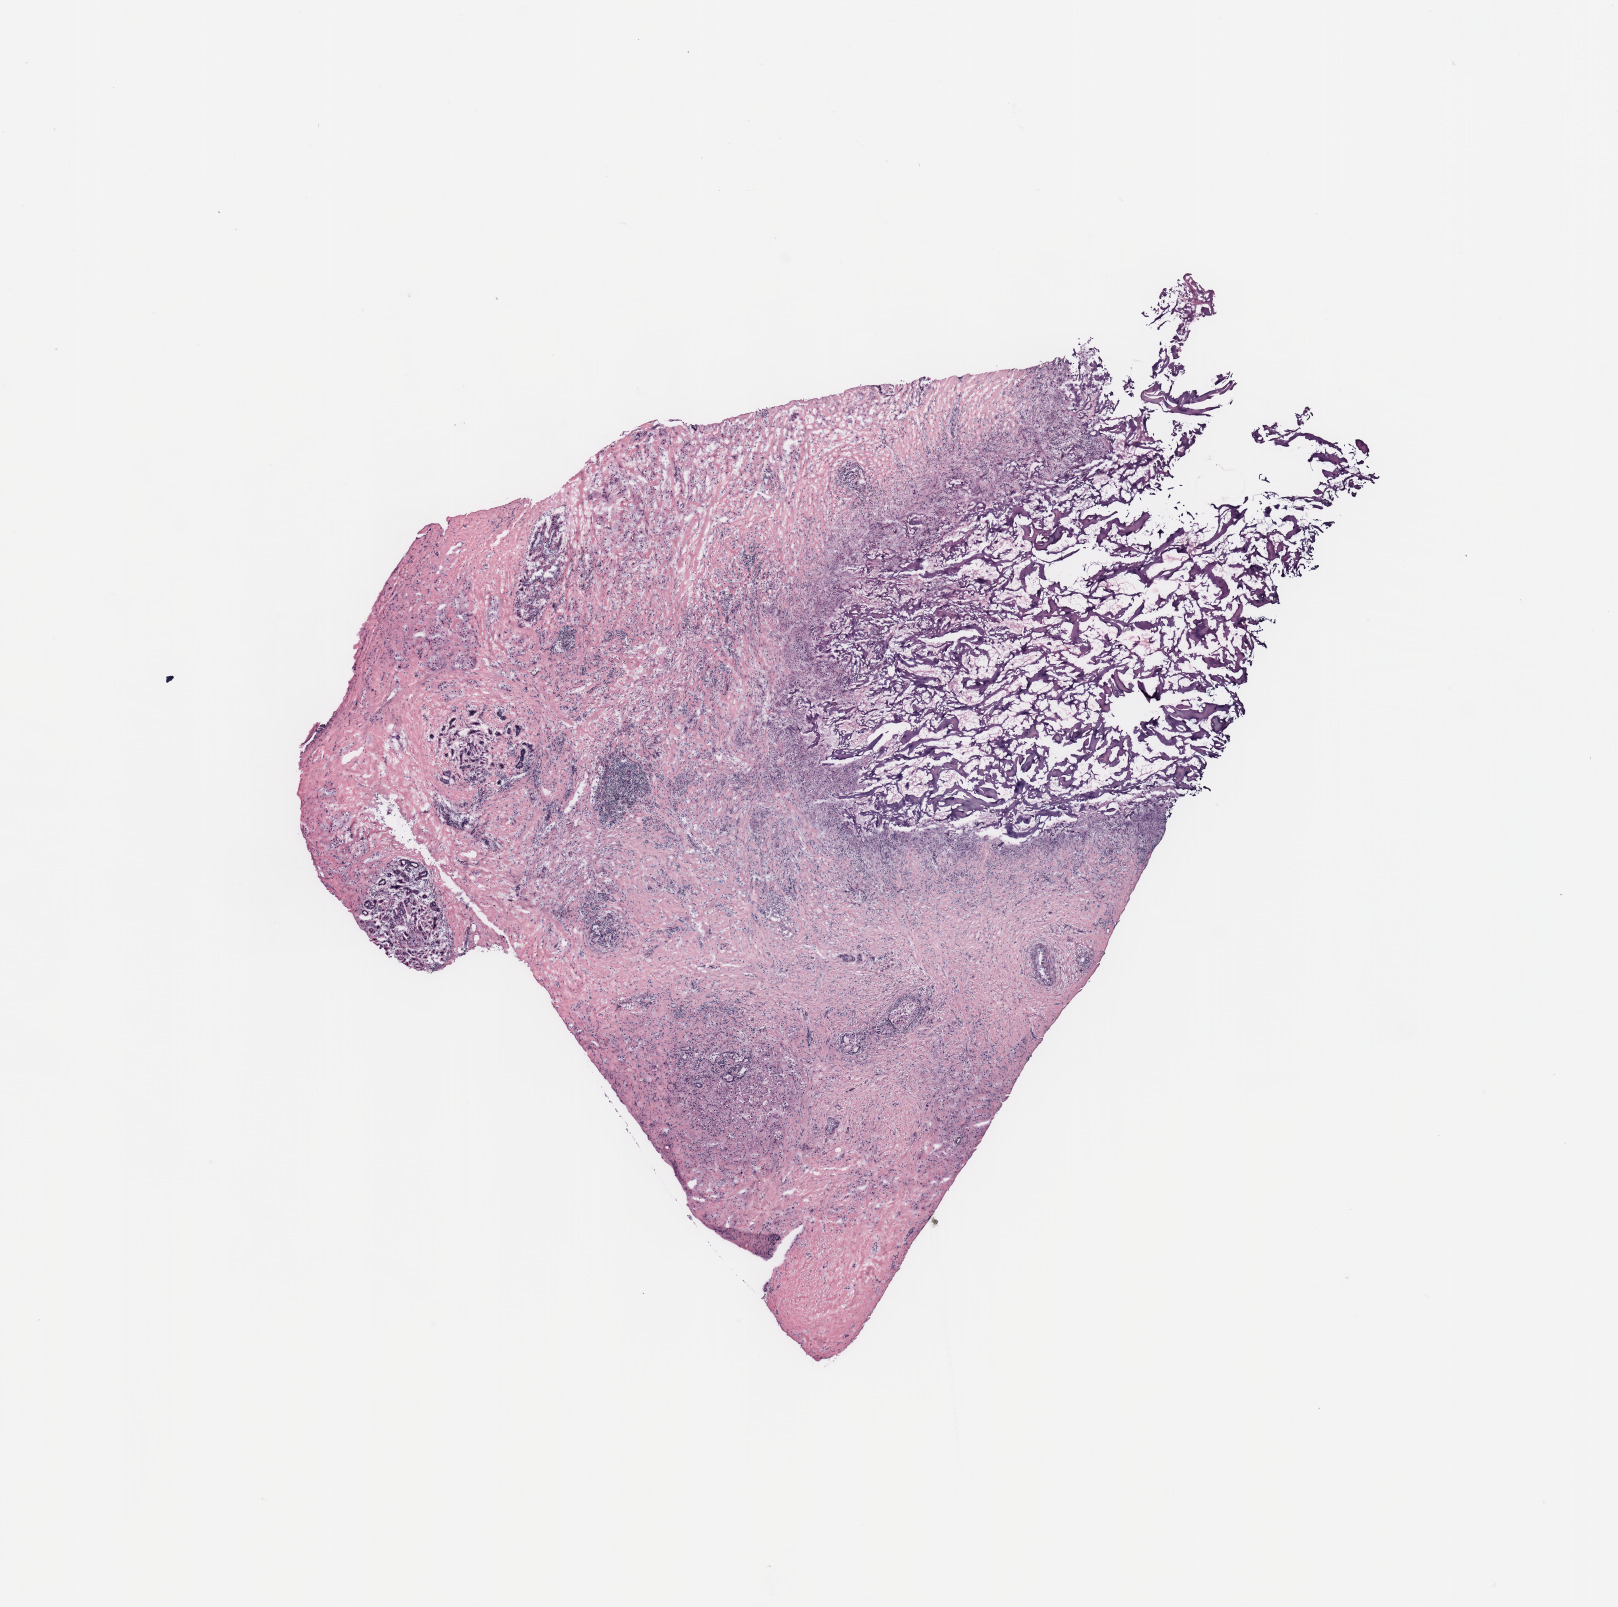
Digitized H&E tissue section (whole slide) — a low-resolution overview of the entire scanned area, about 12.8 x 12.7 mm (slide scanned at 20x), breast, tissue type not recorded.
• patient diagnosis (cohort enrolment): breast cancer (breast)